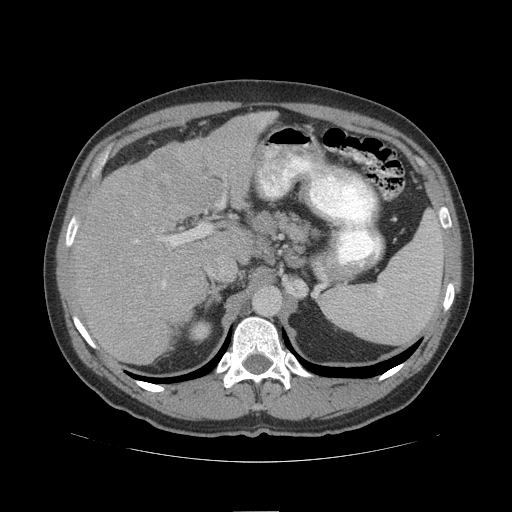
Contrast-enhanced abdominal CT (liver protocol), one axial slice; slice 67 of 109 in the series (ordered by position); reconstruction kernel STANDARD; 140 kVp; soft-tissue window (W 400 / L 40 HU); 2.5 mm slice thickness; 512 × 512 image matrix, field of view 420 × 420 mm. Case-level facts recorded for this patient, not image findings: diagnosis: hepatocellular carcinoma (patient treated with transarterial chemoembolisation; whether this scan precedes or follows treatment is not stated here); TNM stage (as recorded): Stage-IIIB.
Outlined on this slice (semi-automatic segmentation, software-assisted and operator-edited):
- liver parenchyma outside the tumour (the mass and vessels are separate outlines, so this box may not span the whole liver): bounding box (x1, y1, x2, y2) in pixels: (72, 110, 278, 364)
- mass: (146, 141, 222, 213)
- liver vessels: (136, 200, 224, 287)